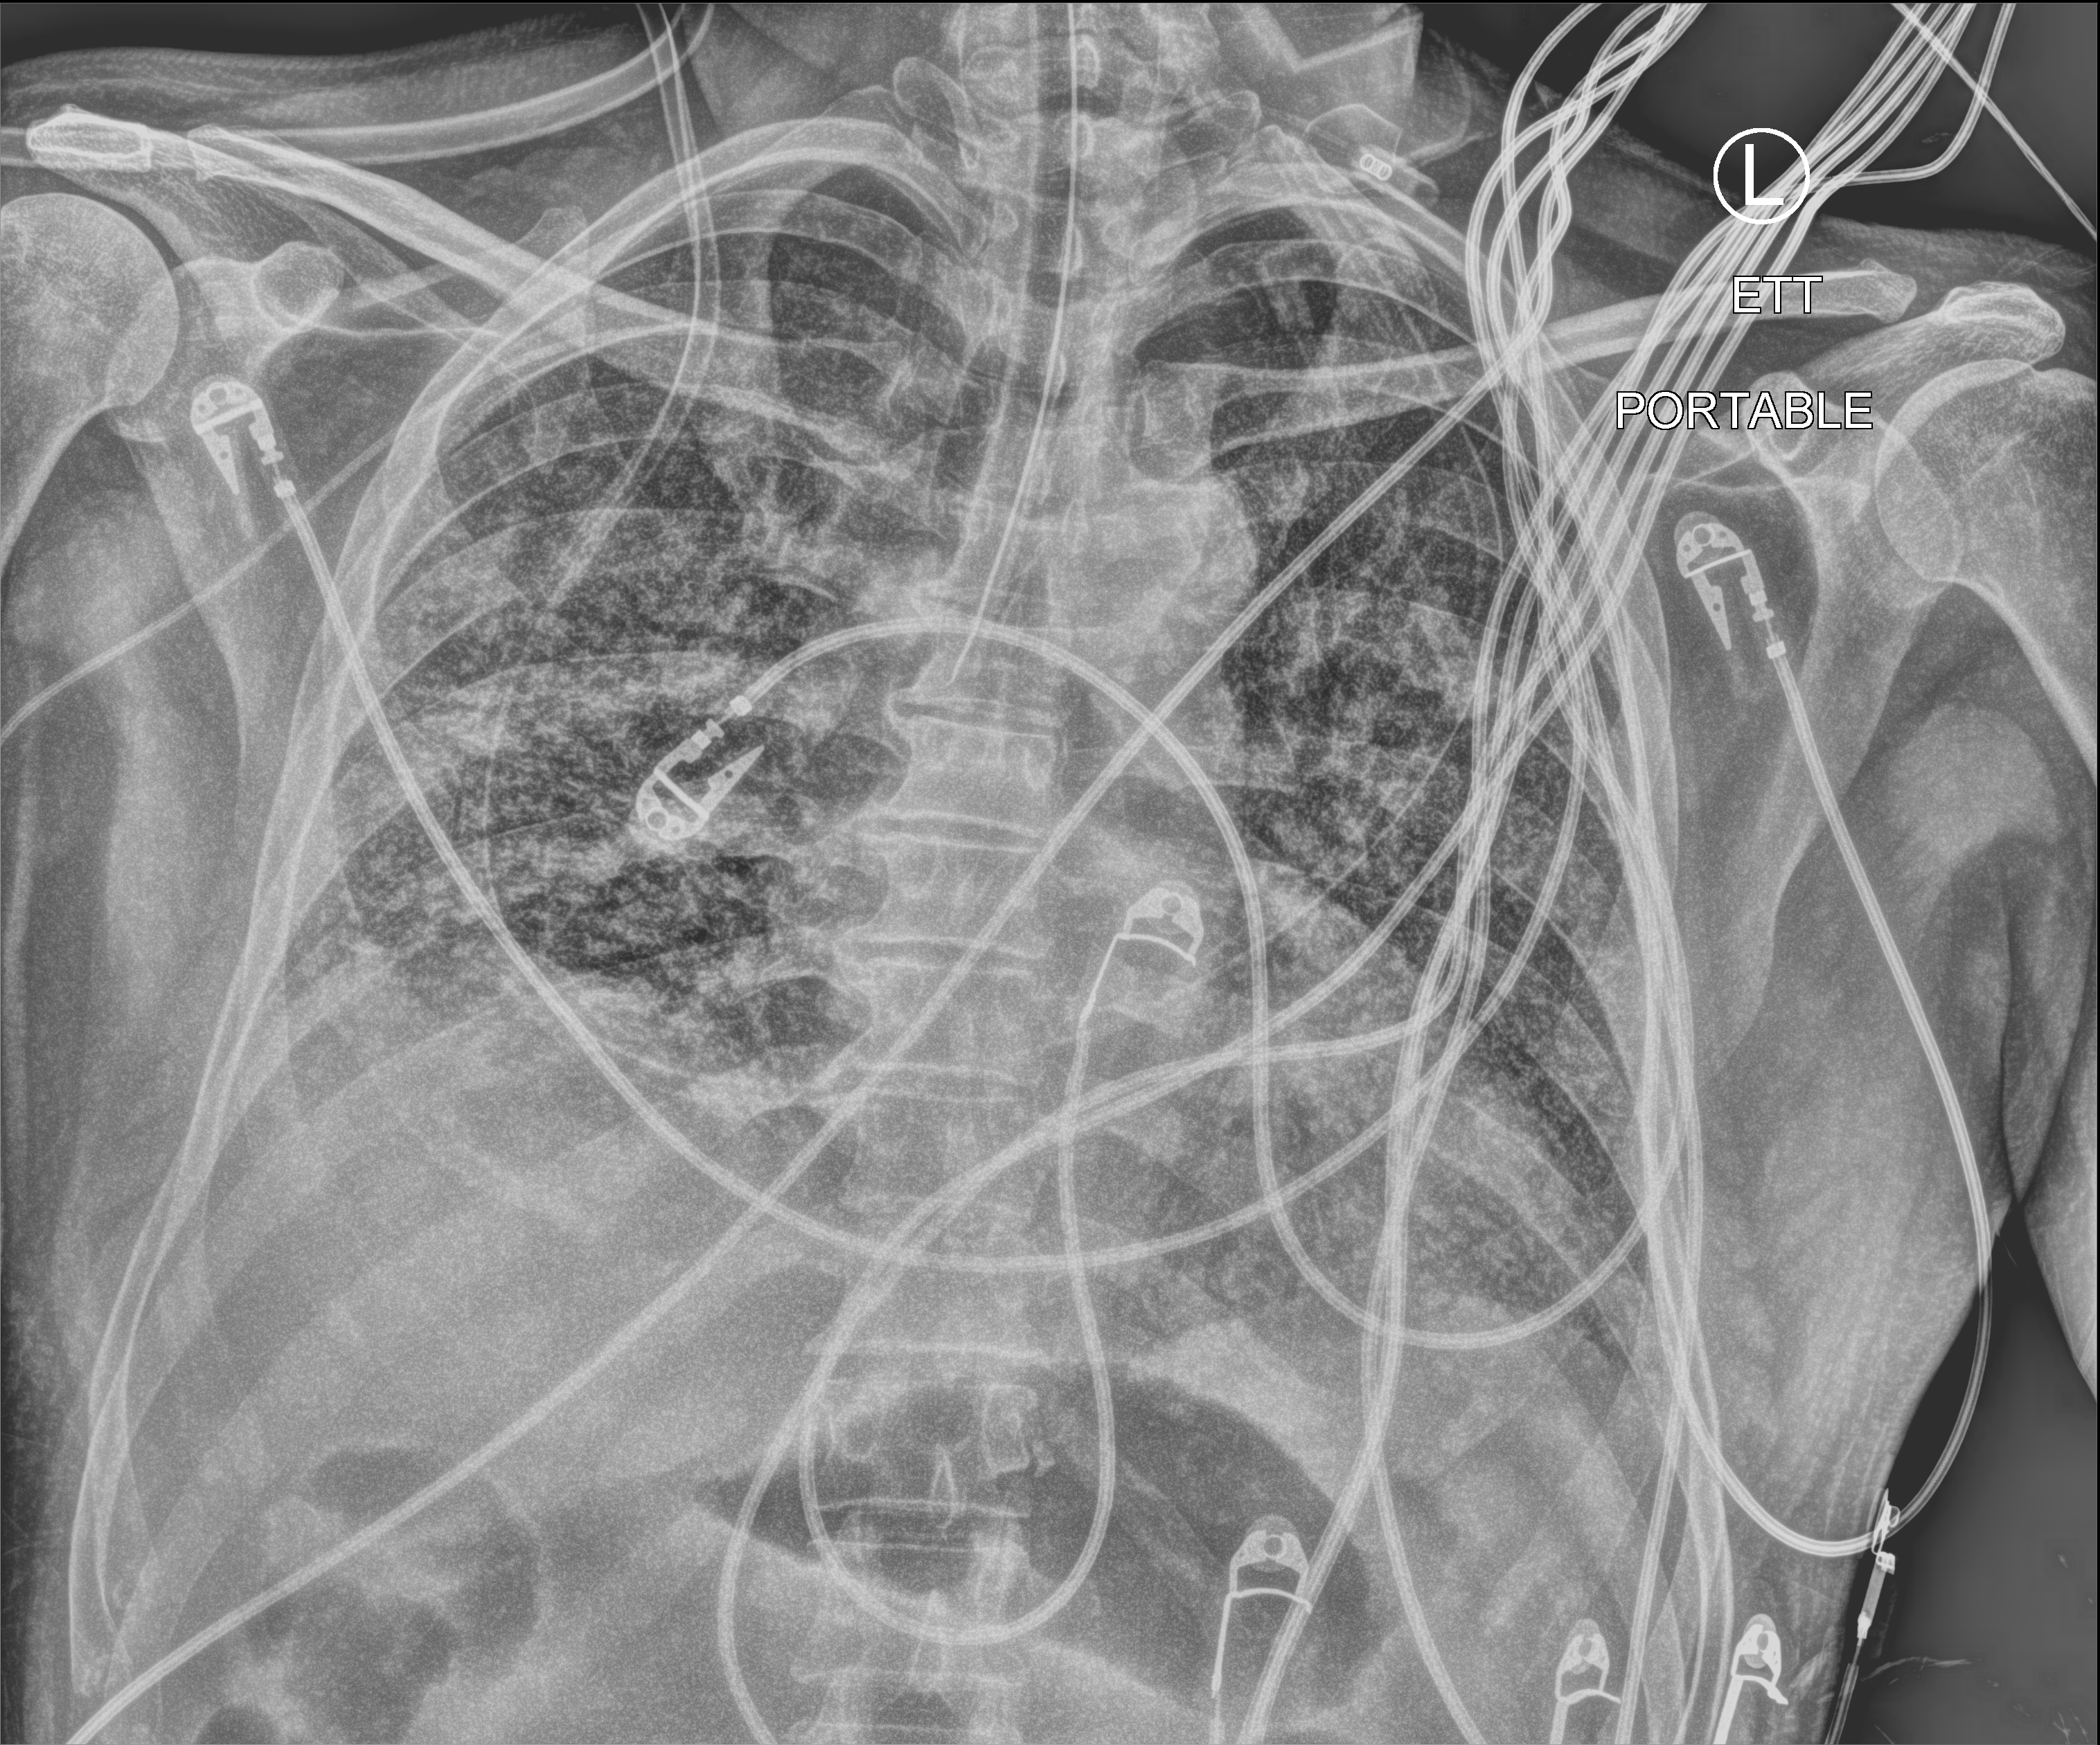
Chest X-ray (portable). Male patient hospitalised with COVID-19, age 18–59 years.
Admission-level facts for this patient (not findings on this image; timing relative to this image not recorded): admitted to intensive care during this hospital stay: yes.